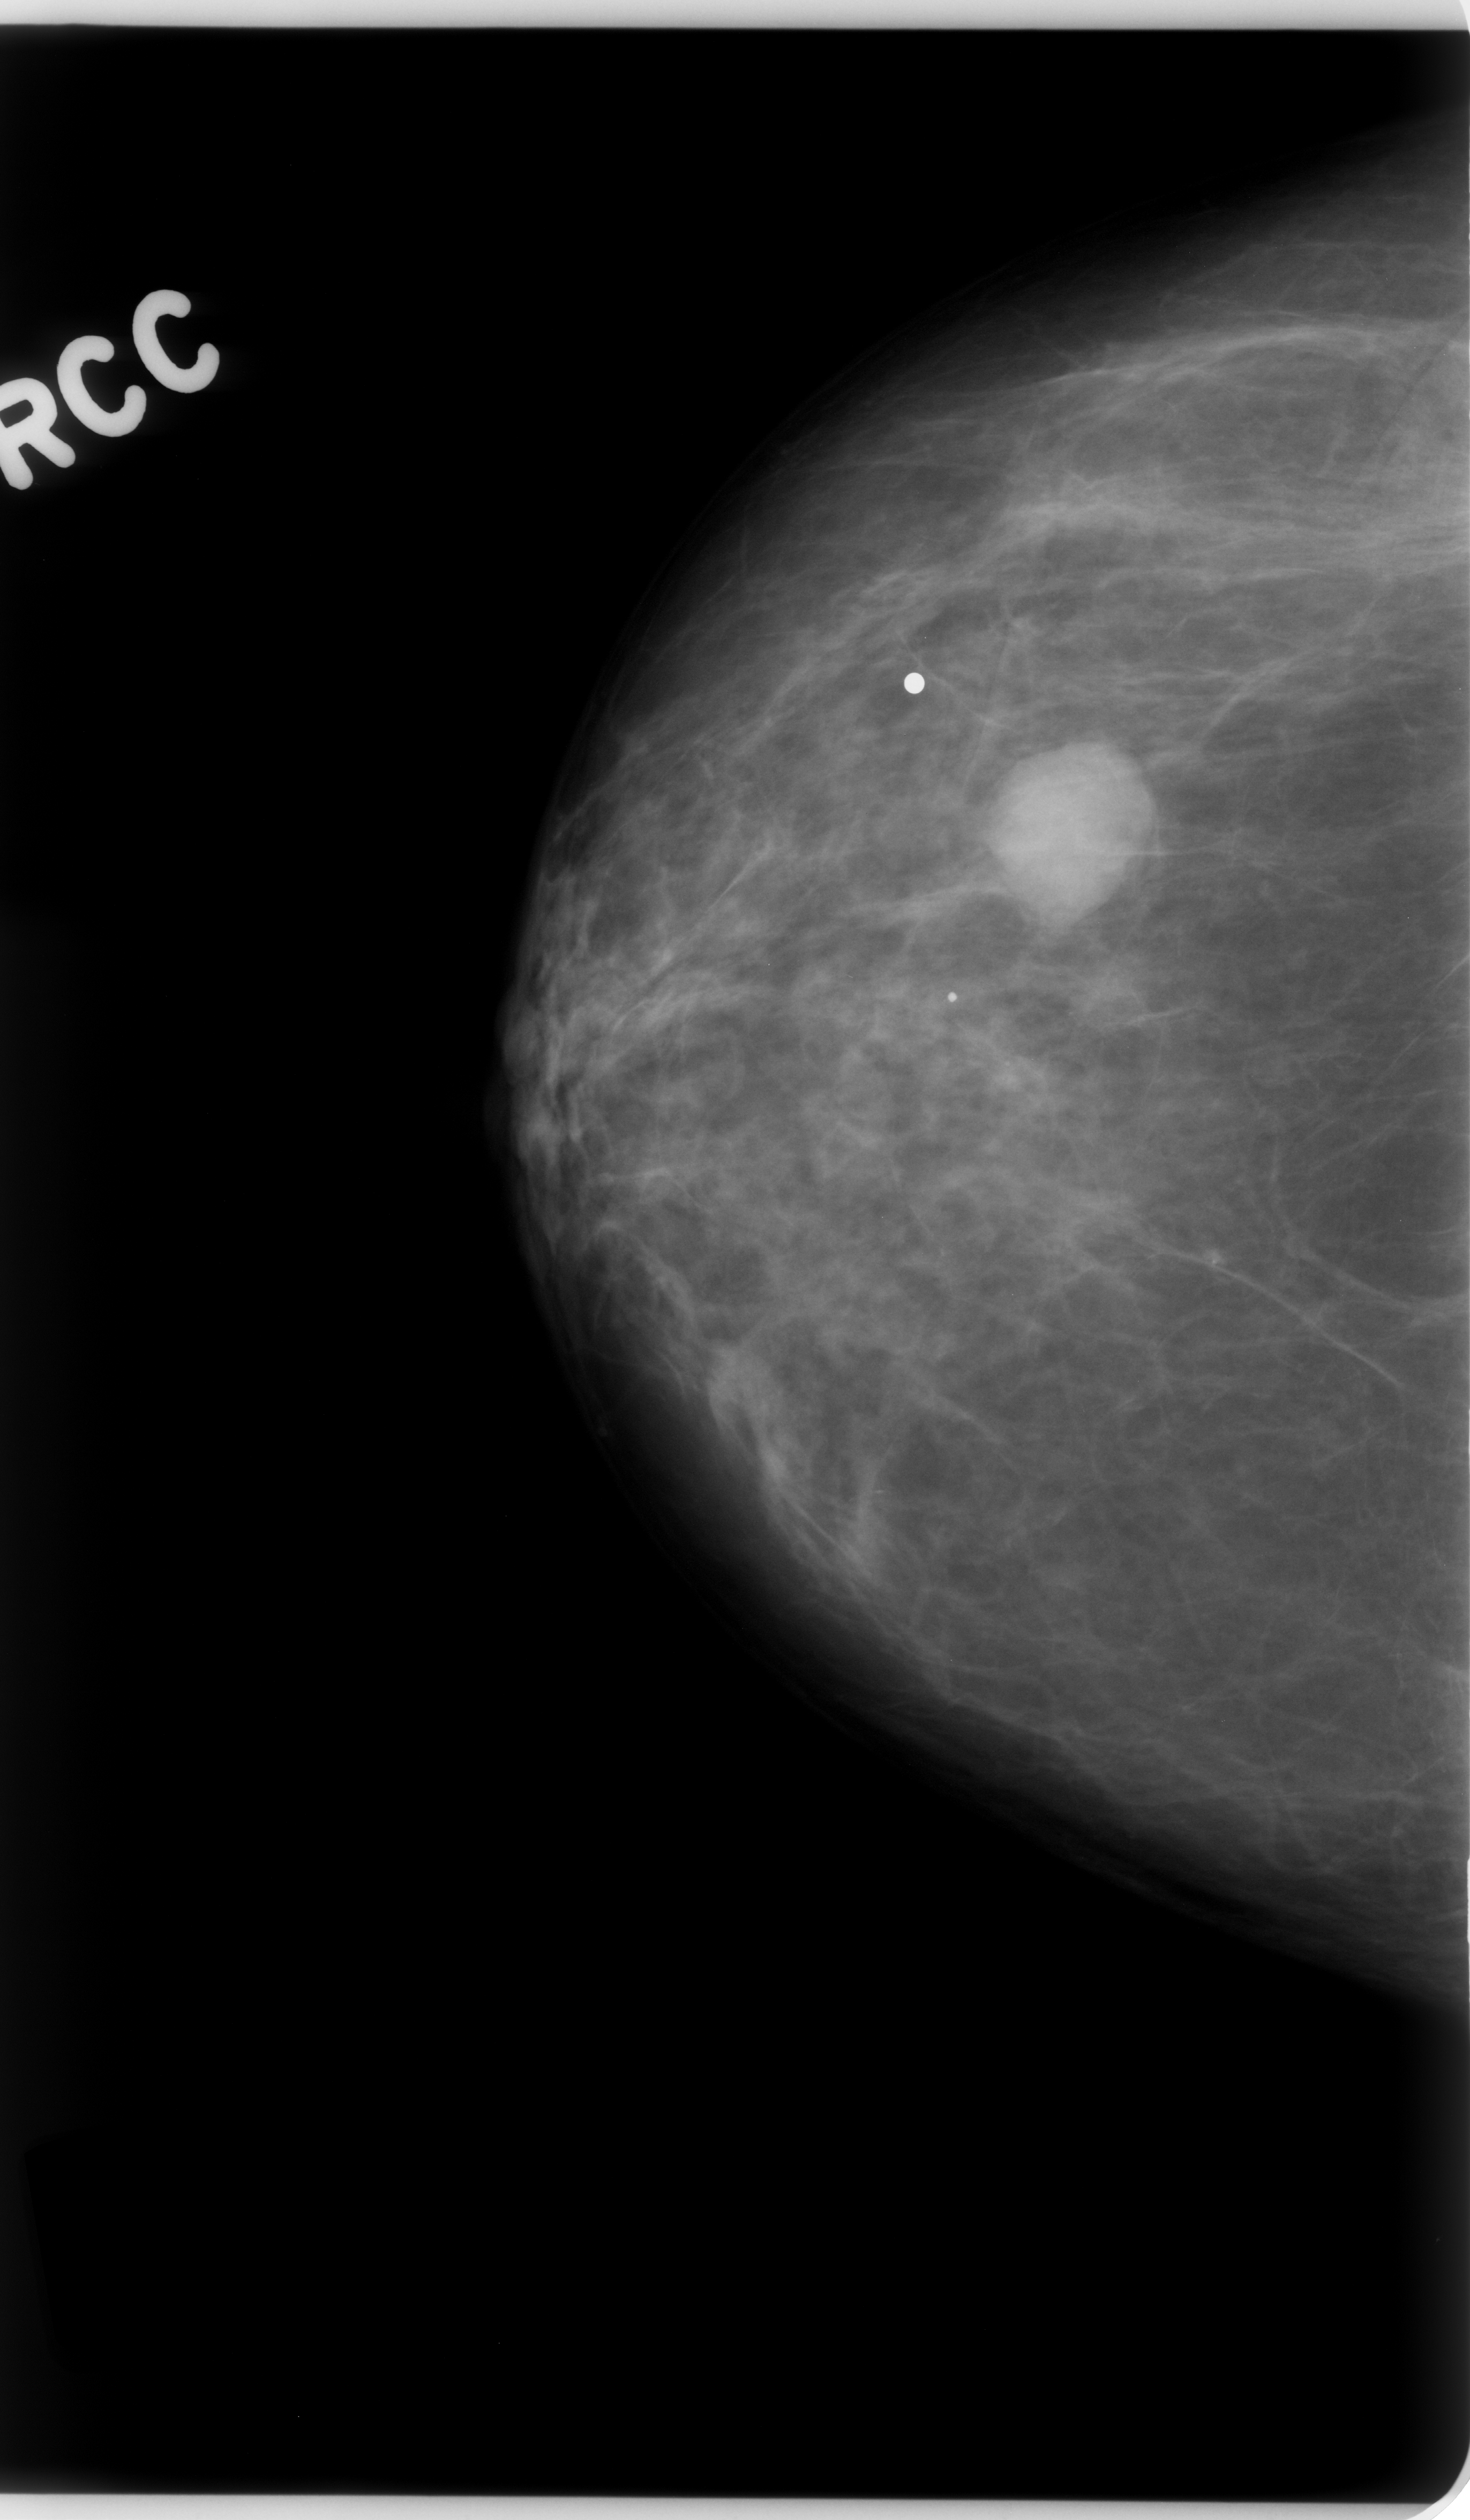
Digitized screen-film mammogram, right breast, craniocaudal (CC) view, breast composition: scattered fibroglandular densities (BI-RADS density category 2 of 4).
- Marked abnormality: mass, shape round, margins circumscribed; BI-RADS assessment category 4; subtlety rating 5 on a 1 (subtle) to 5 (obvious) scale; pathology (as recorded): benign.